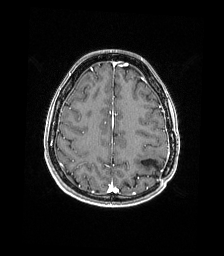
Brain MRI from a brain-tumour surgery series, one axial slice. Position 54 of 176 along the scan axis. T1-weighted post-contrast. 1 mm slice thickness. 224 × 256 image matrix, field of view 224 × 256 mm. Case-level facts recorded for this patient, not image findings: histopathology: Atypical meningioma; WHO grade: 2; tumour location: Paramedian Left Parietal.
Annotated regions visible in this slice (manually delineated by an expert):
- previous resection cavity: bounding box (x1, y1, x2, y2) in pixels: (141, 159, 159, 171)